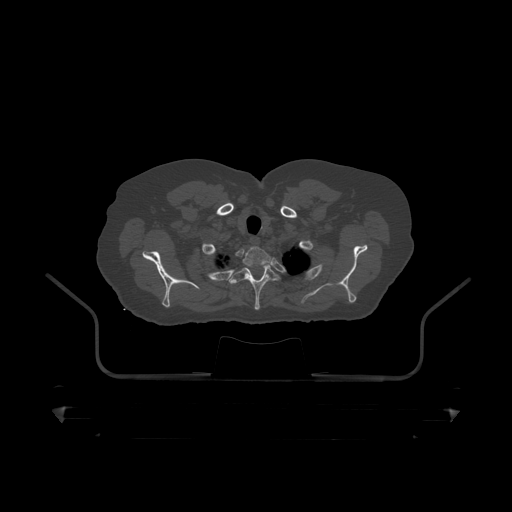
CT including the spine, one axial slice; slice 380 of 390 in the series (ordered by position); reconstruction kernel STANDARD; 120 kVp; bone window (W 1800 / L 400 HU); 1.25 mm slice thickness; 512 × 512 image matrix, field of view 650 × 650 mm. Patient: male, 60 years. From the clinical record (not read from this slice): primary cancer: prostate.
Structures marked on this image (semi-automatic segmentation, software-assisted and operator-edited):
- T1 vertebra: bounding box (x1, y1, x2, y2) in pixels: (213, 246, 271, 267)
- T2 vertebra: (229, 264, 279, 311)